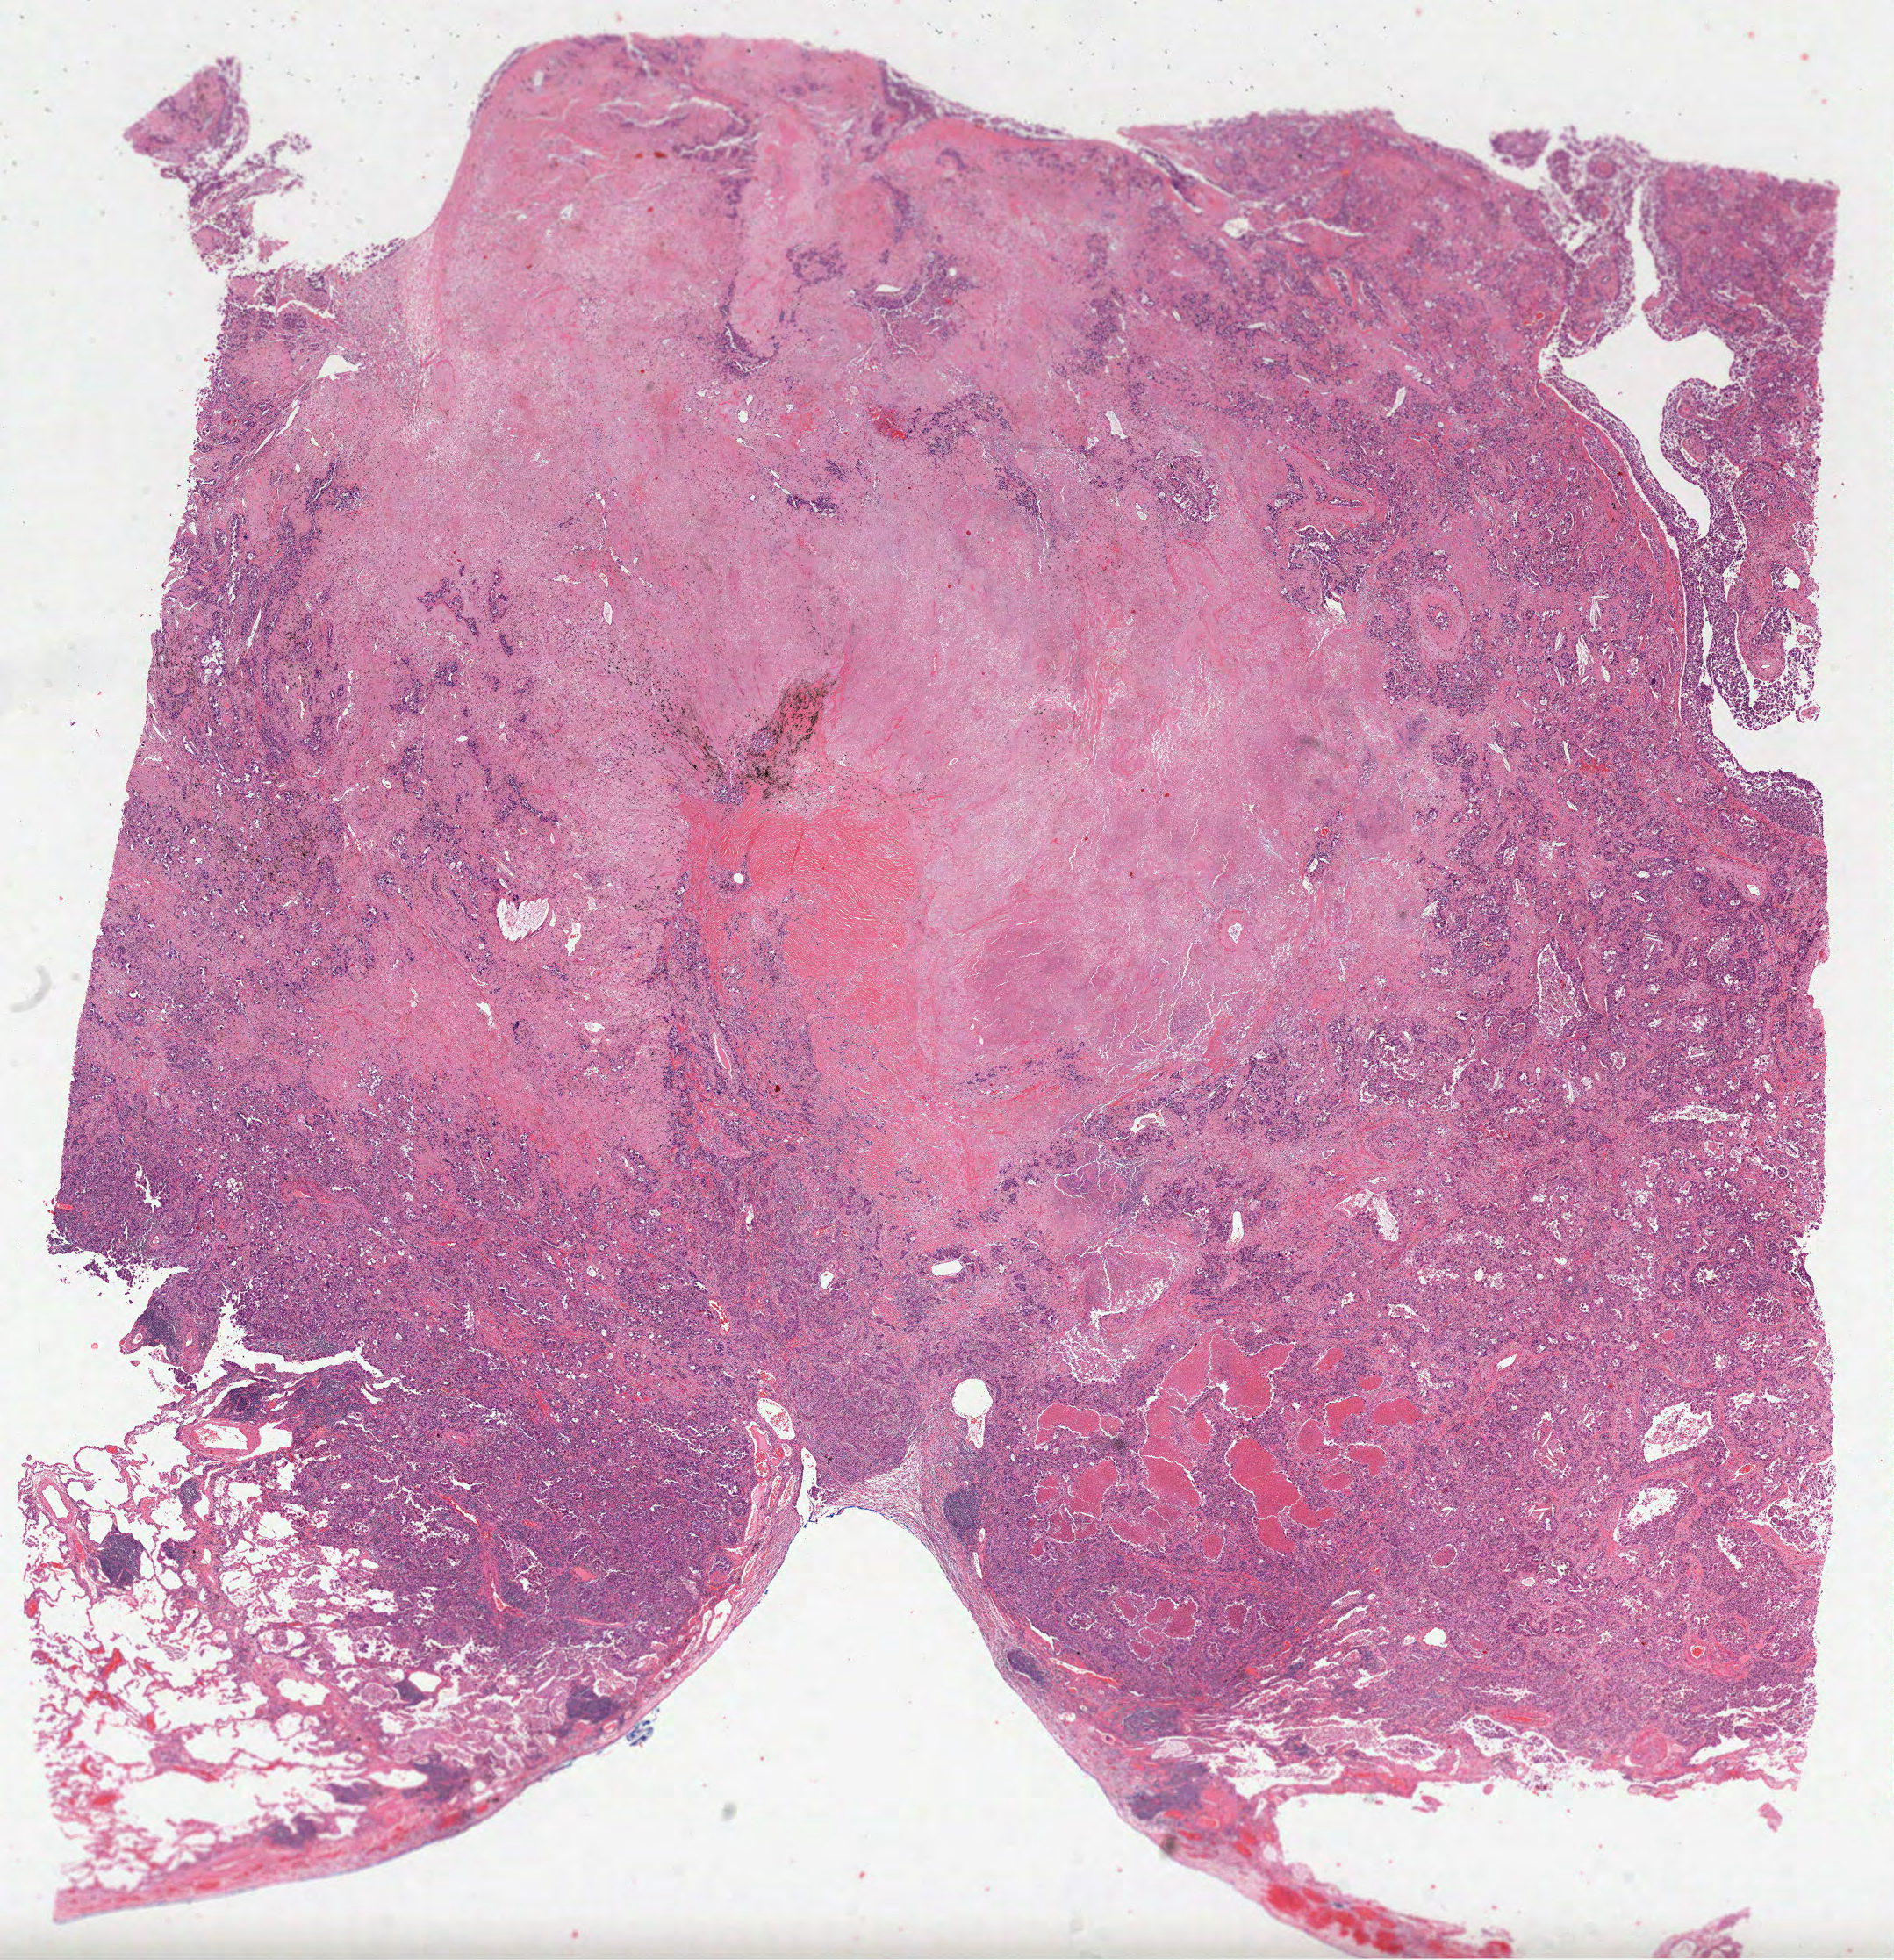
H&E-stained whole-slide image — whole scanned area (about 17.4 x 18.0 mm) shown as a low-resolution overview; formalin-fixed paraffin-embedded (FFPE) diagnostic section; sample: primary tumour, lung. Patient: female, age at initial diagnosis 71 years.
Laterality: right. AJCC pathologic stage: IB. Diagnosis: Acinar cell carcinoma.